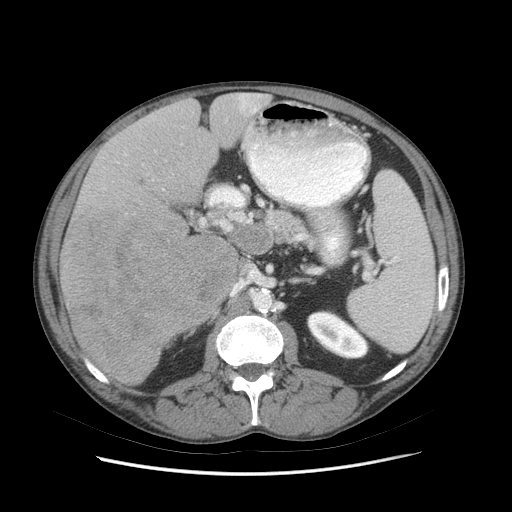
Contrast-enhanced abdominal CT (liver protocol), one axial slice; reconstruction kernel STANDARD; soft-tissue window (W 400 / L 40 HU); 2.5 mm slice thickness; 512 × 512 image matrix, field of view 380 × 380 mm. Case-level facts recorded for this patient, not image findings: diagnosis: hepatocellular carcinoma (patient treated with transarterial chemoembolisation; whether this scan precedes or follows treatment is not stated here); TNM stage (as recorded): Stage-IIIB; Child-Pugh class: A; tumour nodularity: multinodular.
Annotated regions visible in this slice (semi-automatic segmentation, software-assisted and operator-edited):
- liver parenchyma outside the tumour (the mass and vessels are separate outlines, so this box may not span the whole liver): bounding box <60,92,270,384> (left, top, right, bottom; pixels)
- mass: <60,205,235,383>
- liver vessels: <162,93,261,190>